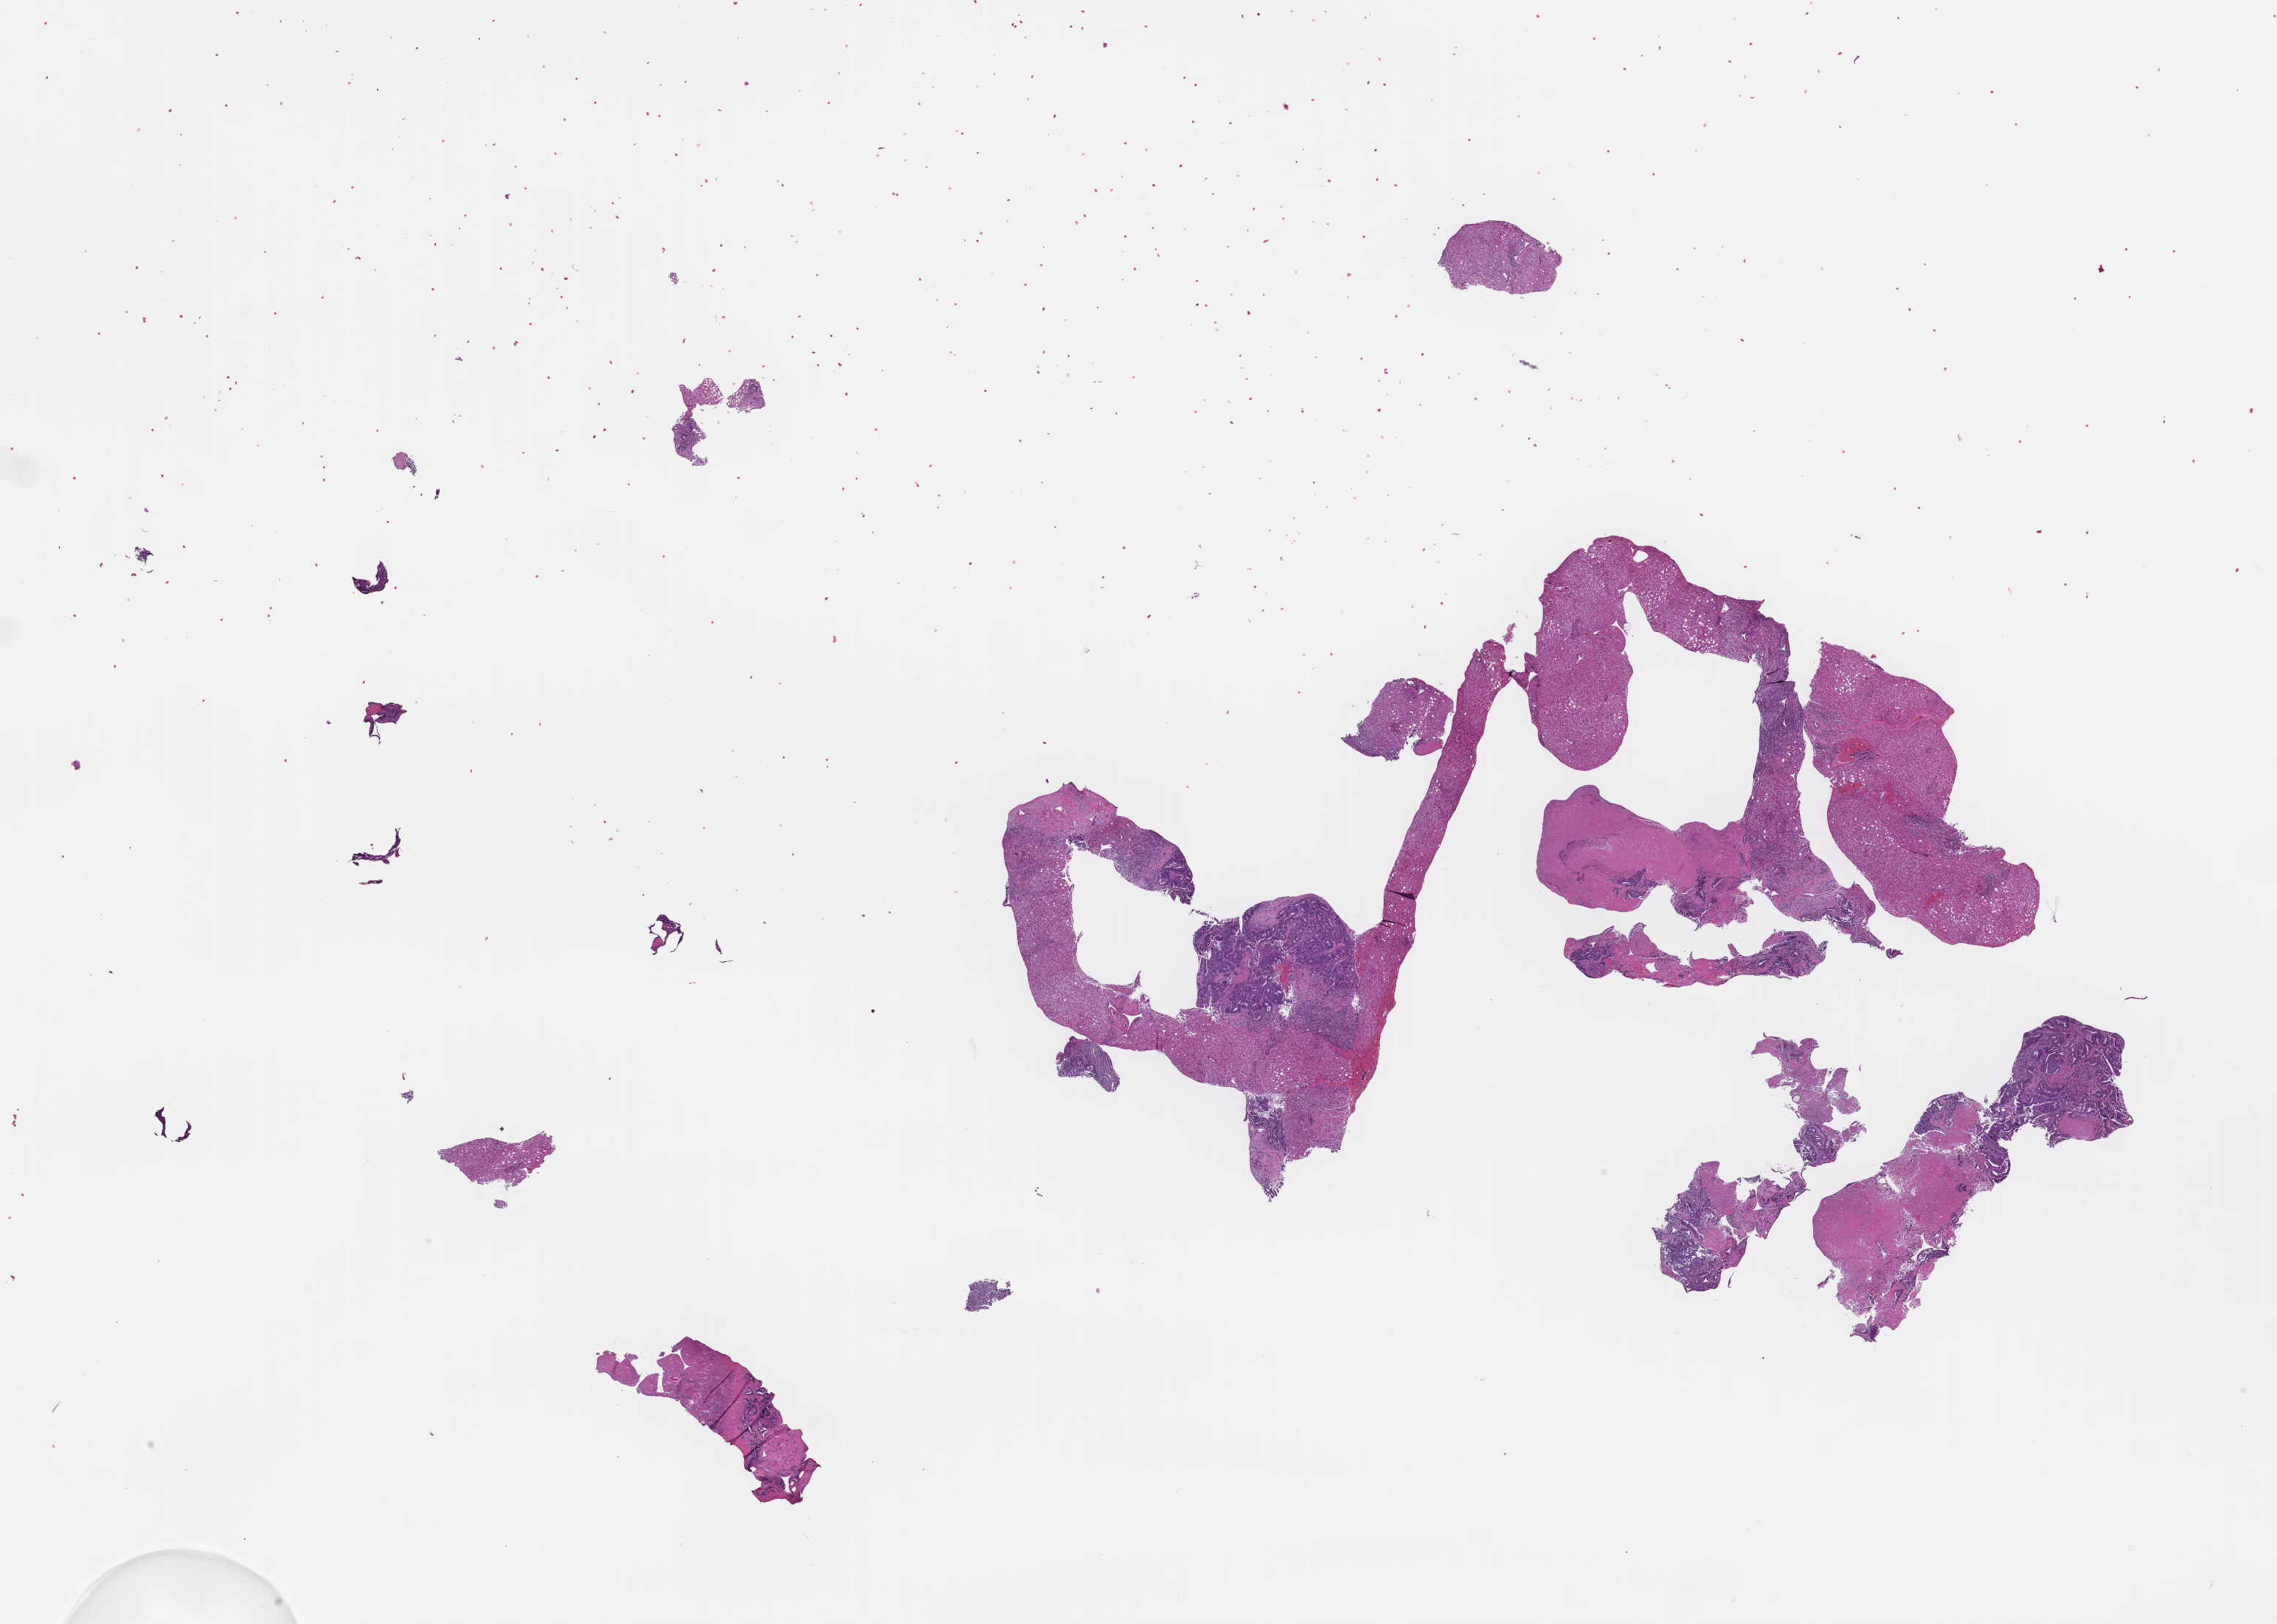
Whole-slide image, H&E stain — low-resolution overview of the scanned area, about 25.1 x 17.9 mm; formalin-fixed paraffin-embedded section; collected at baseline (before treatment). Female patient.
This section: metastasis (sampled organ not recorded). Patient diagnosis (primary): Colorectal Carcinoma.